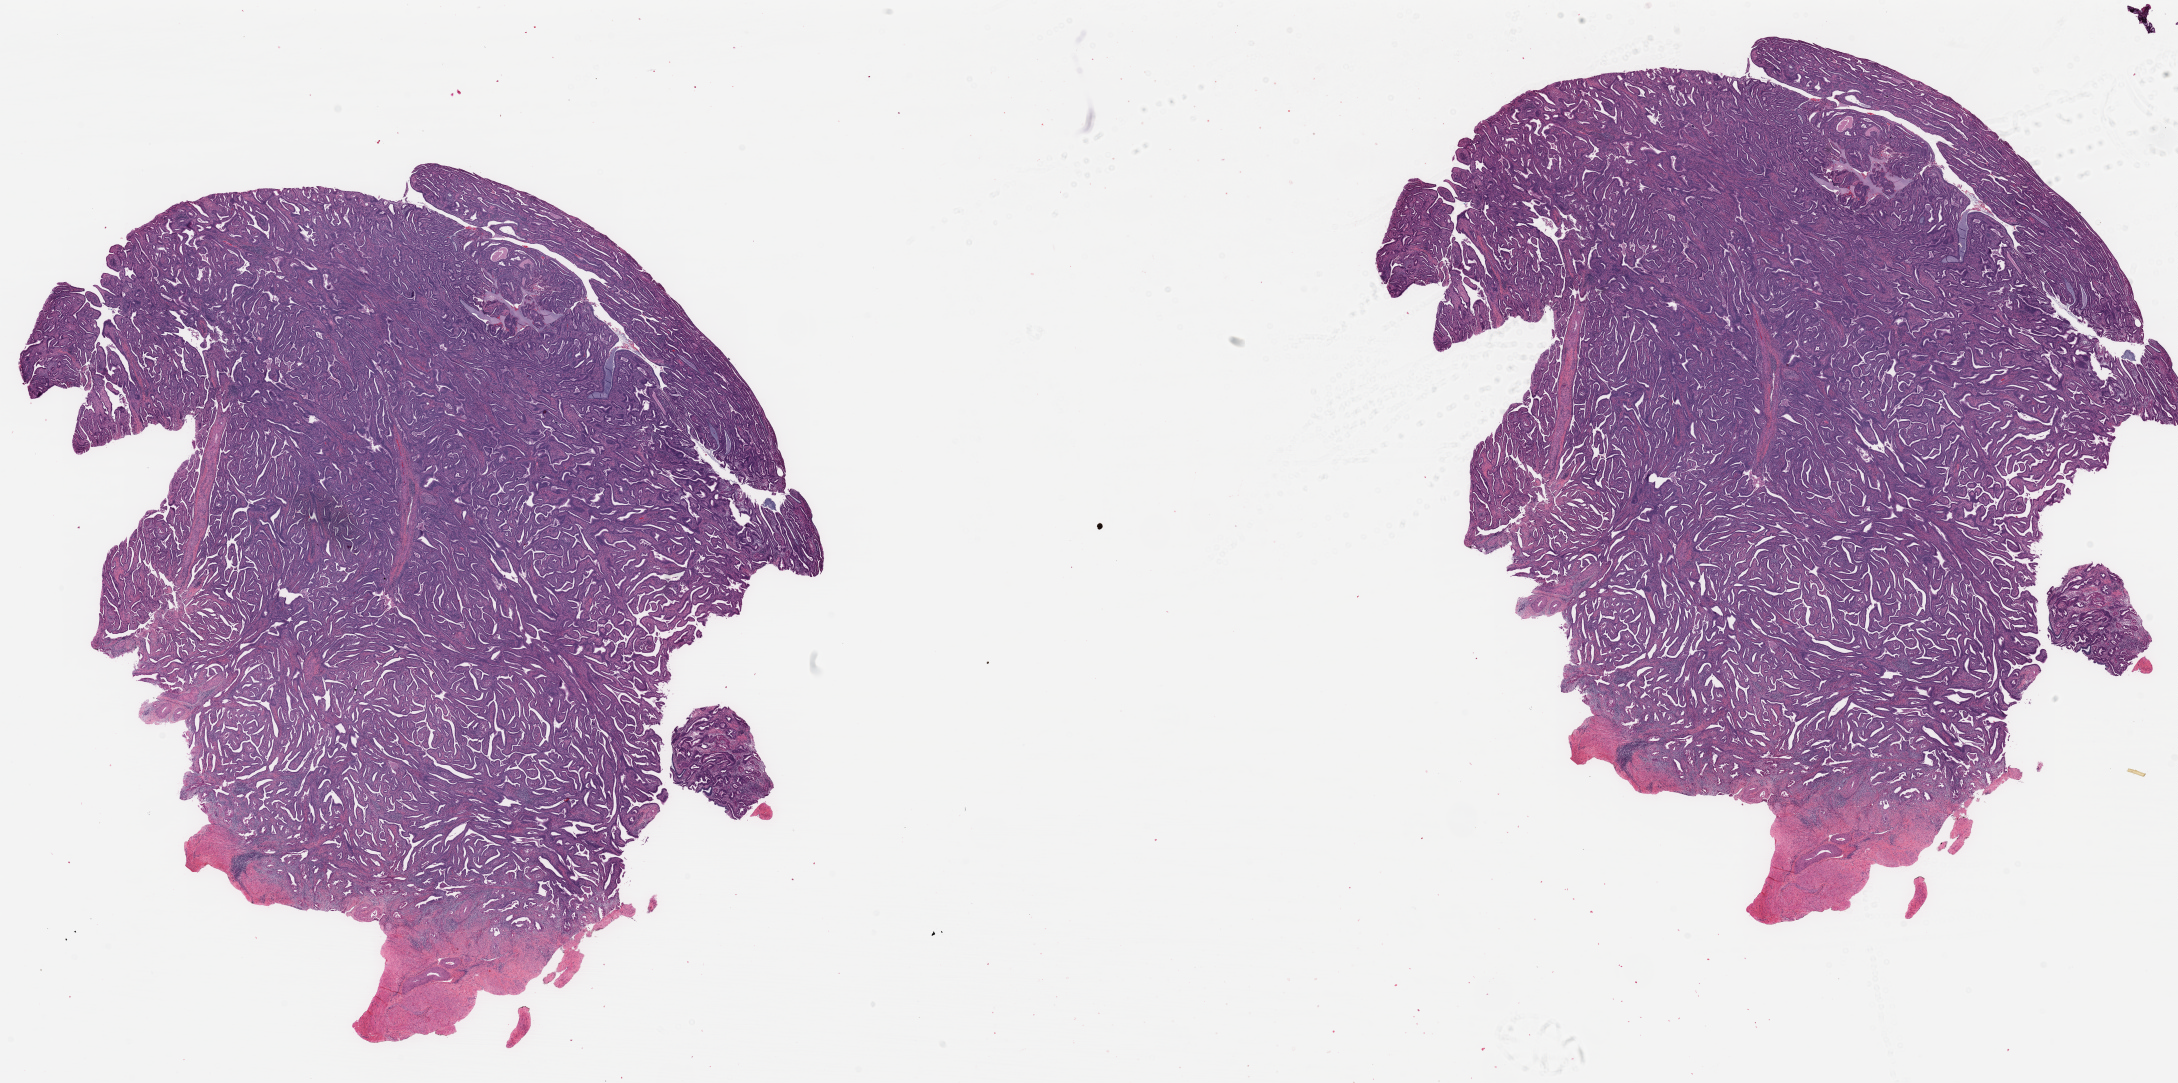
Hematoxylin and eosin (H&E) stained whole-slide image — shown as a low-resolution overview of the whole scanned area (about 34.5 x 17.1 mm), formalin-fixed paraffin-embedded (FFPE) diagnostic section, primary tumour sample from the cervix. Patient: female, age at initial diagnosis 38 years.
Diagnosis: Adenocarcinoma, NOS (cervix uteri).